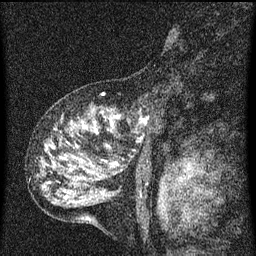
Breast MRI (dynamic contrast-enhanced), one sagittal slice; slice 37 of 60 in the series (ordered by position); dynamic contrast-enhanced series, image 2 of 3 at this slice position (ordered by acquisition); 1.5 T; TE 4.2 ms, TR 8 ms; 2 mm slice thickness; 256 × 256 image matrix, field of view 180 × 180 mm. Patient: female, 55 years.
Structures marked on this image (semi-automatic segmentation, software-assisted and operator-edited):
- analysis volume of interest (the breast-tissue region the enhancement analysis was run in; not a lesion): bounding box (x1, y1, x2, y2) in pixels: (42, 100, 149, 159)
- tumour enhancement mask (voxels above the 70 % enhancement threshold inside the analysis volume of interest): (72, 116, 117, 133)